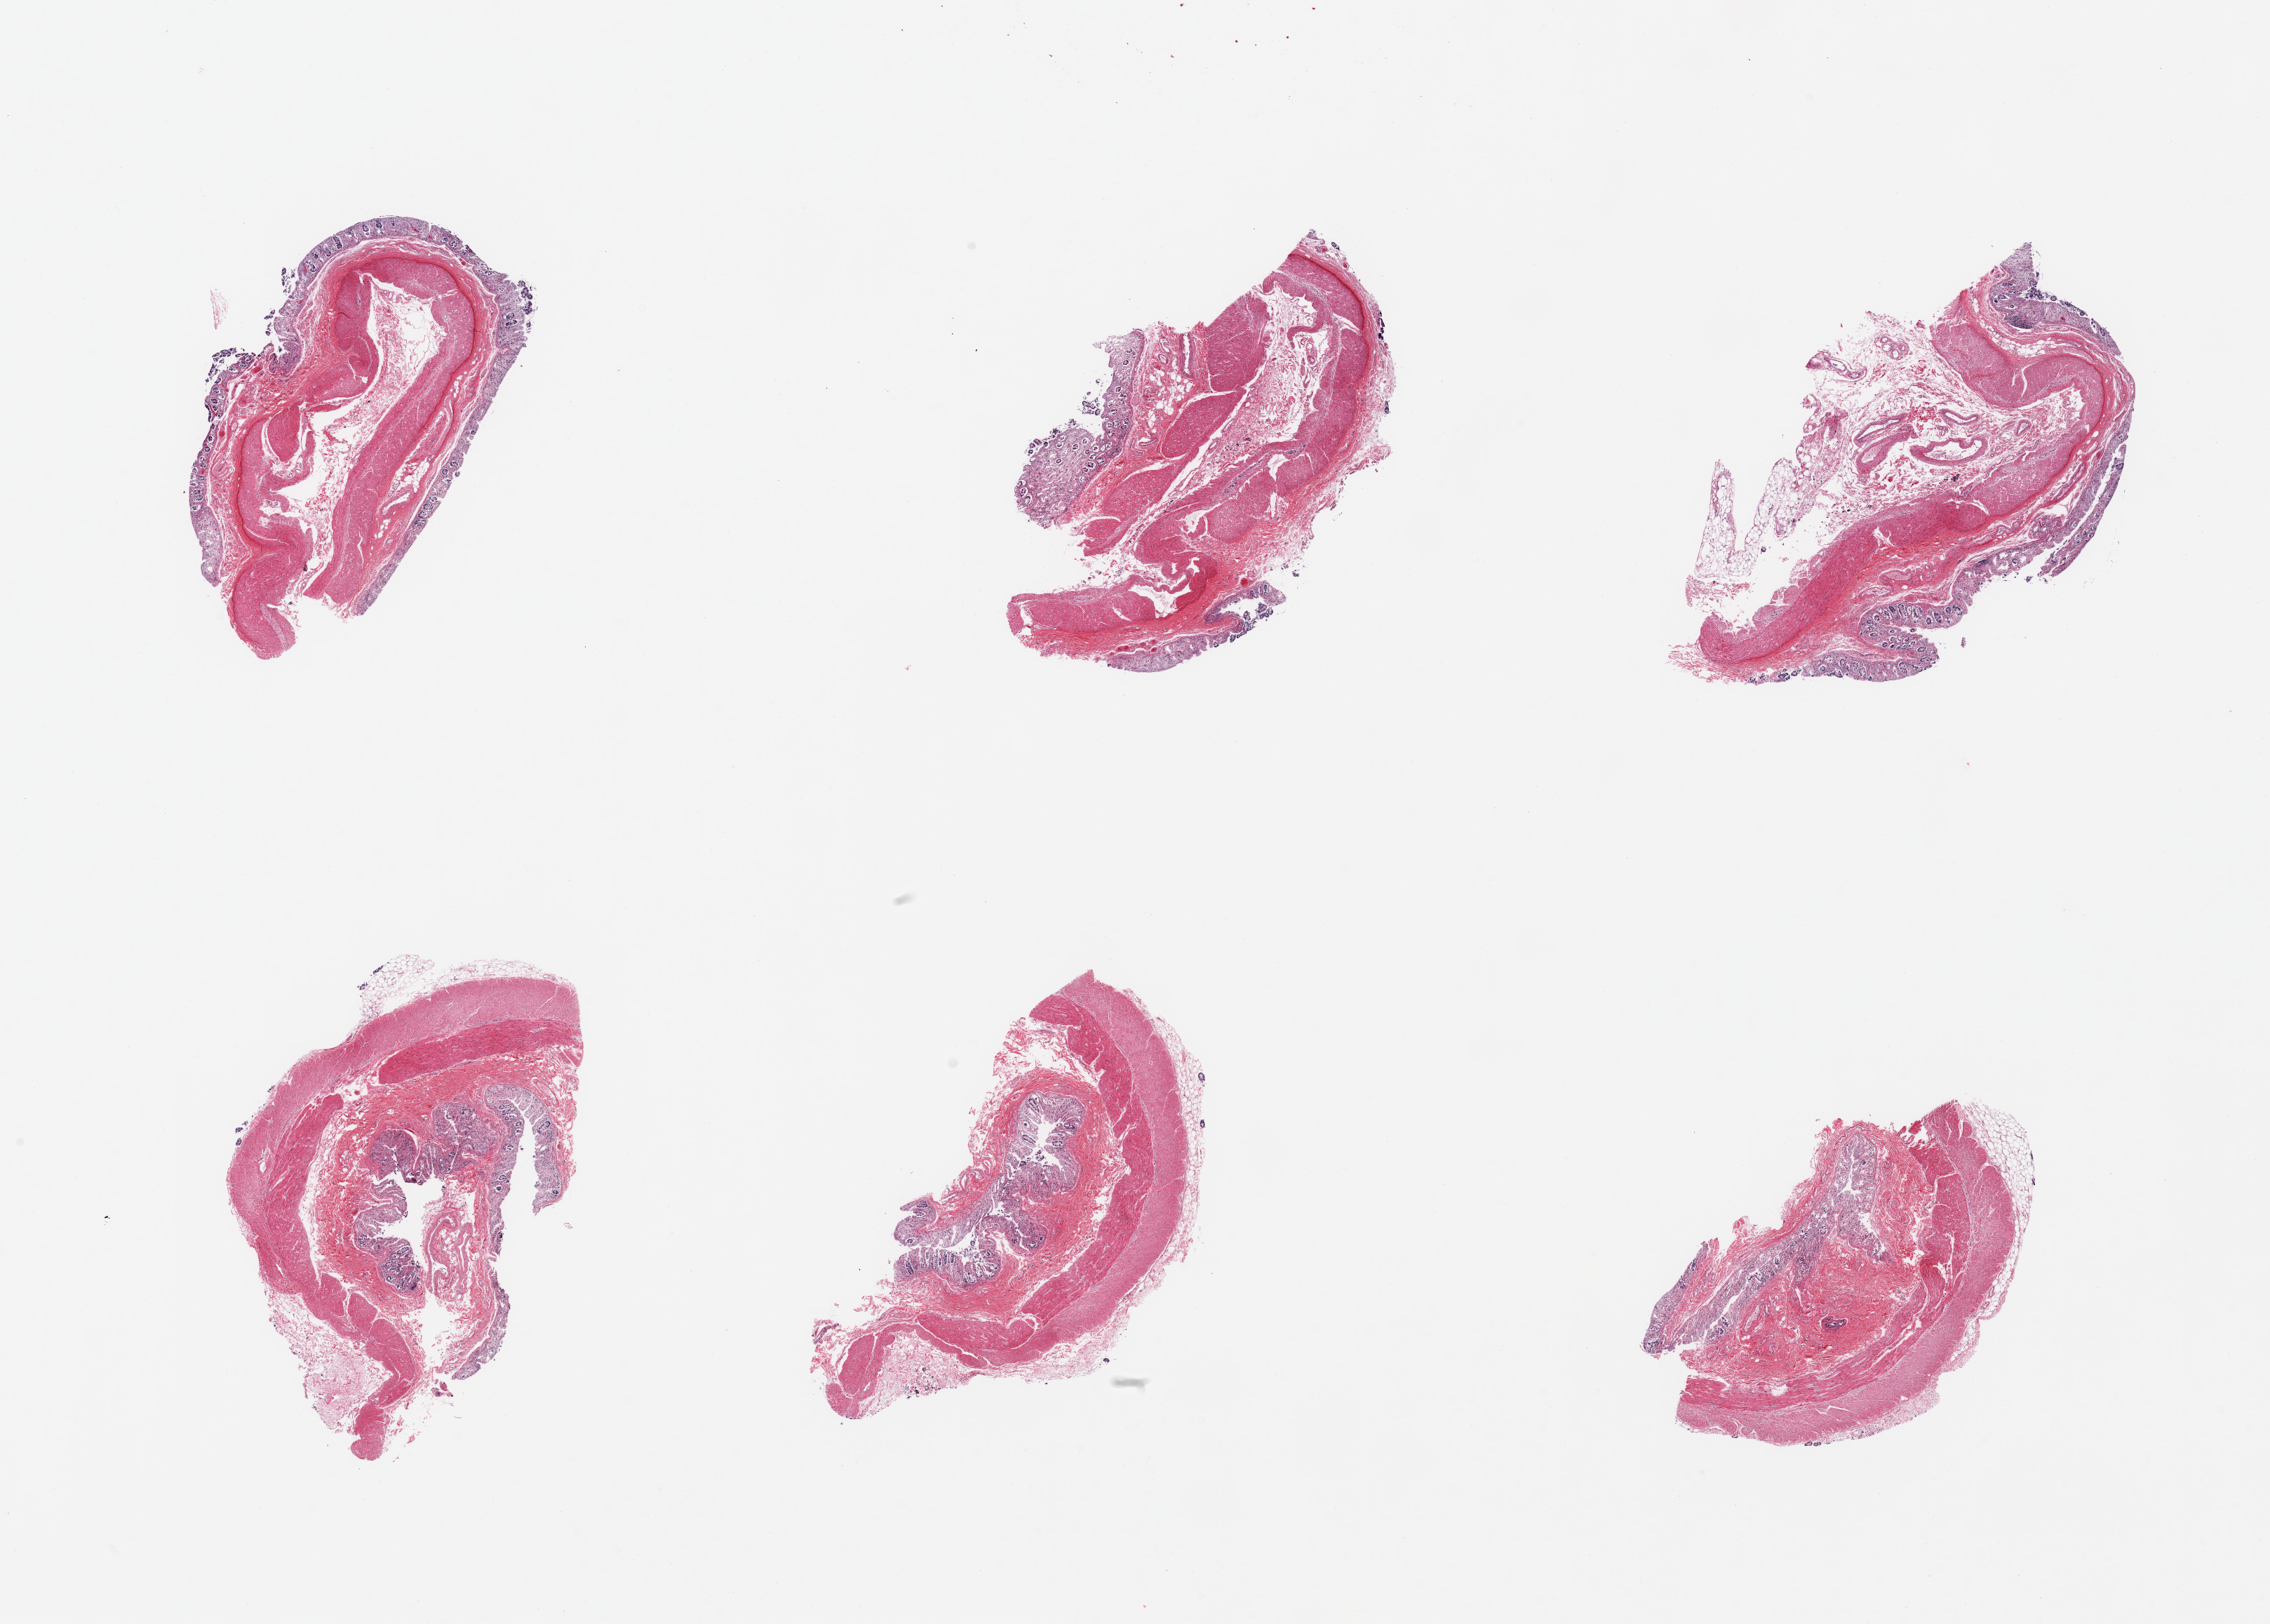
Digitized H&E-stained section, shown as a low-resolution overview of the whole scanned area (about 25.6 x 18.3 mm, from a 20x scan); PAXgene-fixed, paraffin-embedded tissue; section of transverse colon (target tissue); donor tissue sample. Donor: male.
Reviewer comment on this tissue sample: 6 pieces, mucosa up to ~0.2mm, advanced autolysis/sloughing.